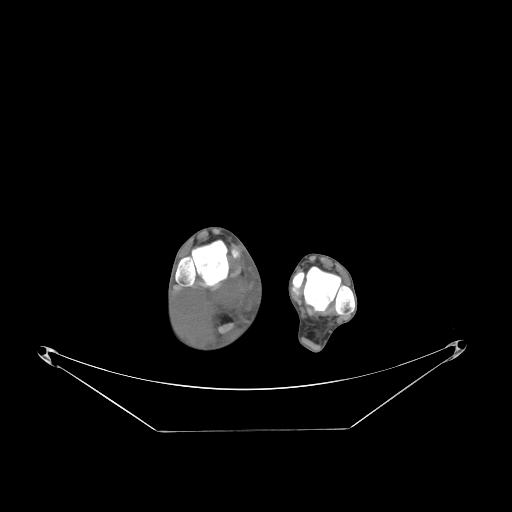
CT of an extremity soft-tissue mass (from a PET/CT study), one axial slice; position 45 of 267 along the scan axis; reconstruction kernel STANDARD; 140 kVp; soft-tissue window (W 400 / L 40 HU); 3.75 mm slice thickness; 512 × 512 image matrix, field of view 500 × 500 mm. Male patient. From the clinical record (not read from this slice): histological type: liposarcoma - round cell; grade: high; site of the primary tumour: right calf.
Annotated regions visible in this slice (expert contour drawn on MRI and transferred to this co-registered scan by the dataset authors):
- gross tumour volume (mass): bounding box [x1, y1, x2, y2] px = [176, 288, 248, 346]